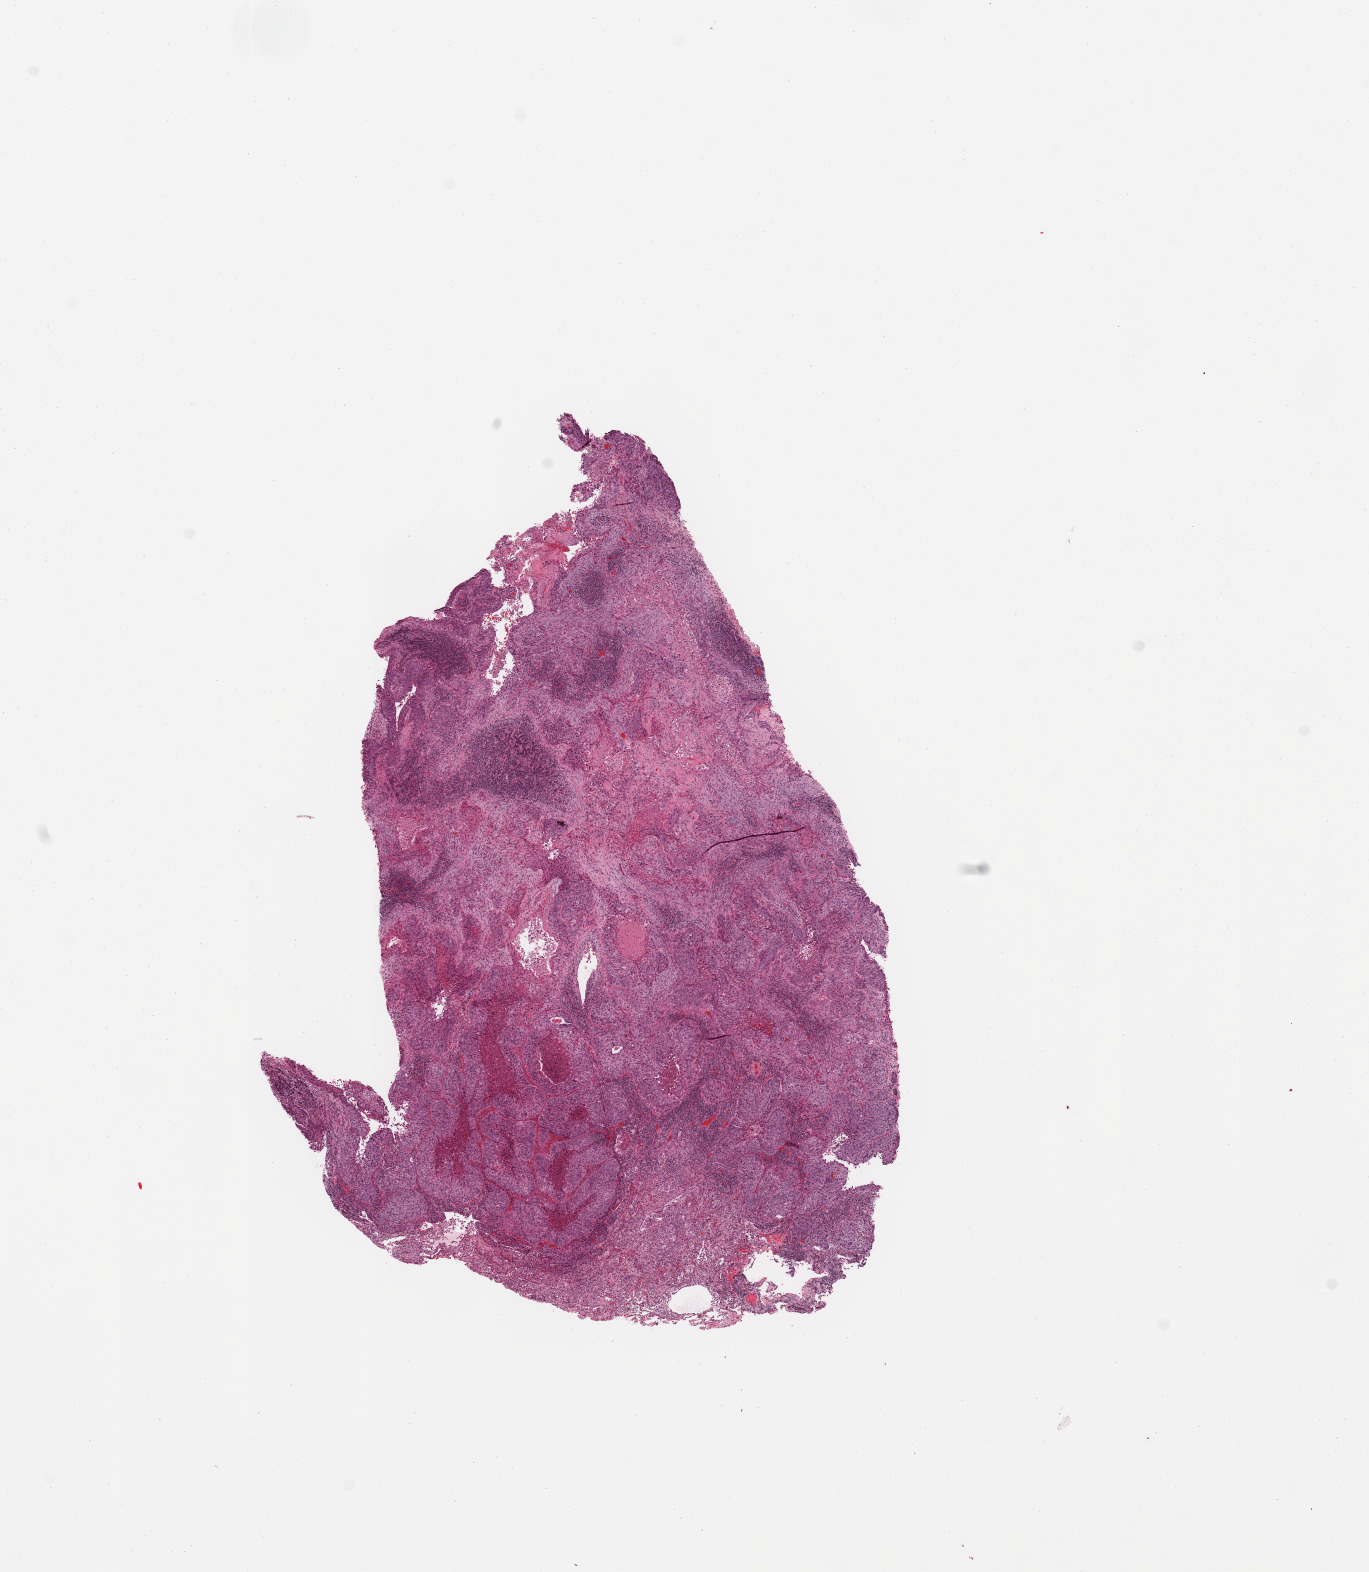
Whole-slide histology image, Hematoxylin and eosin (H&E) stained — whole scanned area (about 10.8 x 12.4 mm, slide scanned at 20x) shown as a low-resolution overview, lung, tumour tissue. 74-year-old male patient. Histologic grade: G2 (moderately differentiated).
AJCC pathologic stage: IA. Primary tumour site (as recorded): right upper lobe. Histologic diagnosis: Squamous cell carcinoma, NOS.